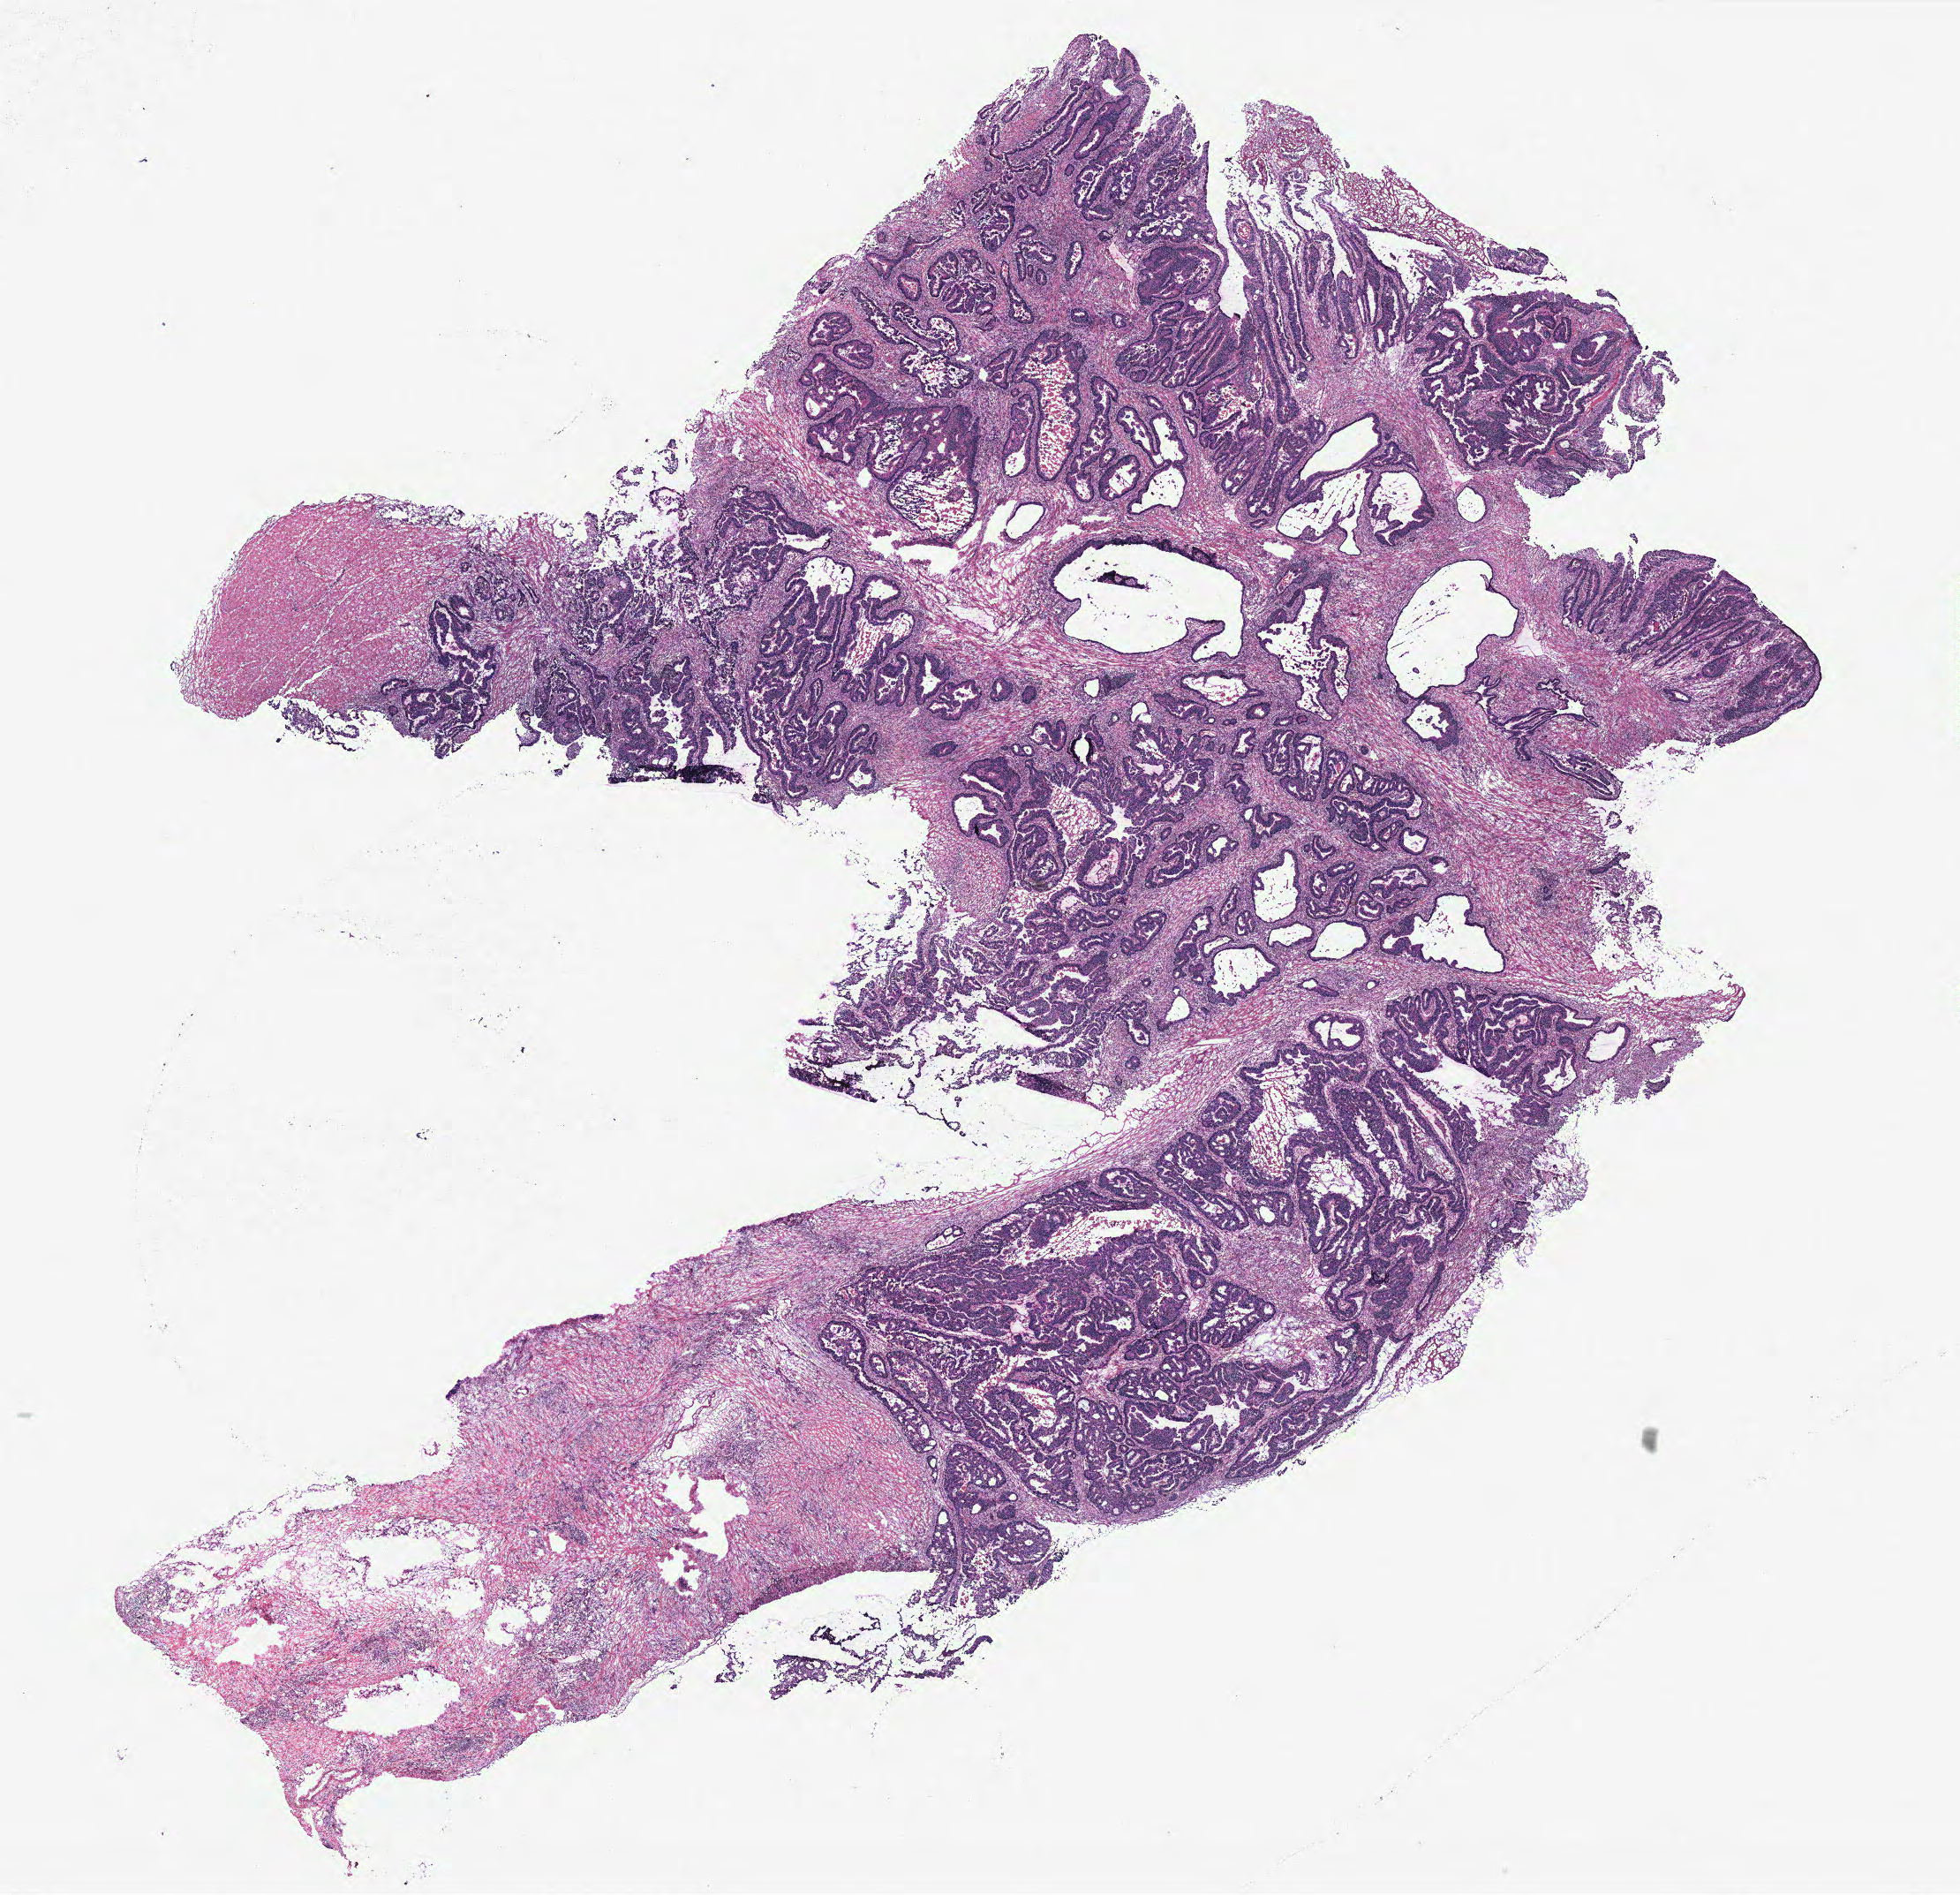
Whole-slide histology image, Hematoxylin and eosin (H&E) stained — low-resolution overview of the scanned area, about 17.8 x 17.2 mm (acquisition: 40x scan), normal (non-tumour) tissue sample, colon. 71-year-old female patient.
This section: normal (non-tumour) tissue from the same patient. Patient diagnosis: Adenocarcinoma, NOS.